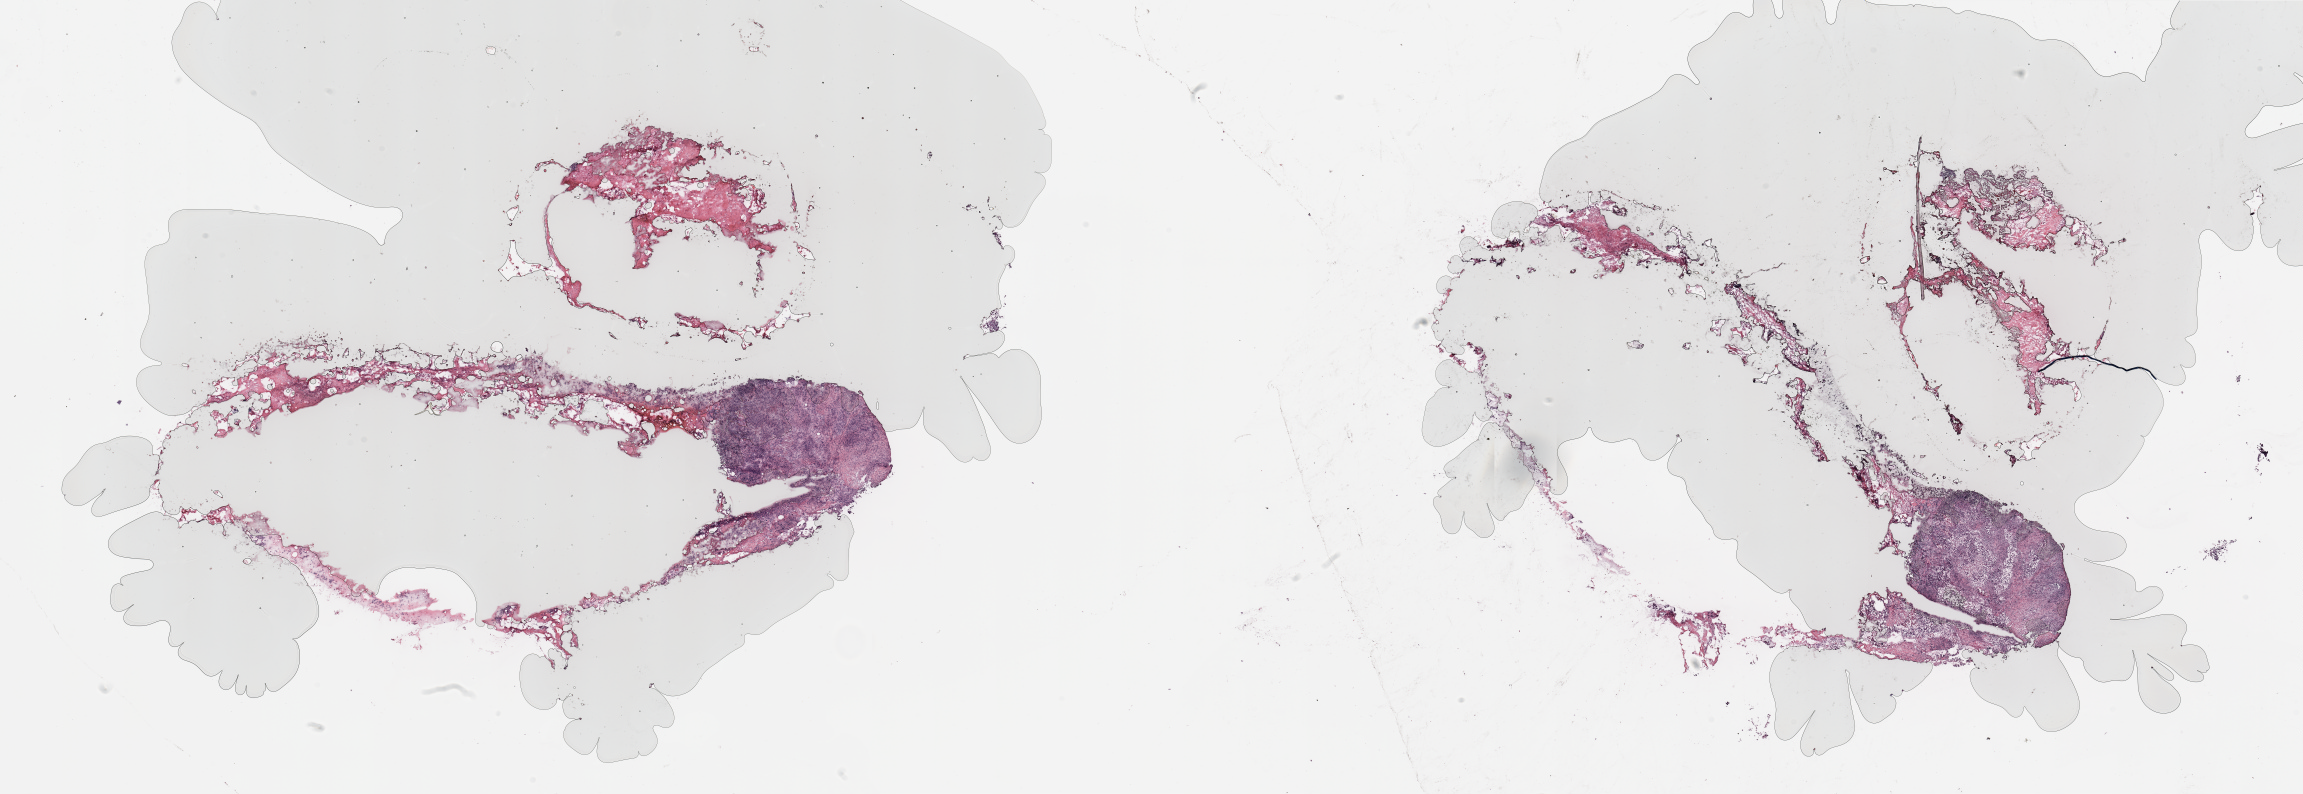
Digitized H&E-stained tissue section (whole slide) — low-resolution overview of the scanned area, about 36.4 x 12.6 mm, breast, tissue type not recorded.
Patient diagnosis (cohort enrolment): breast cancer (breast).